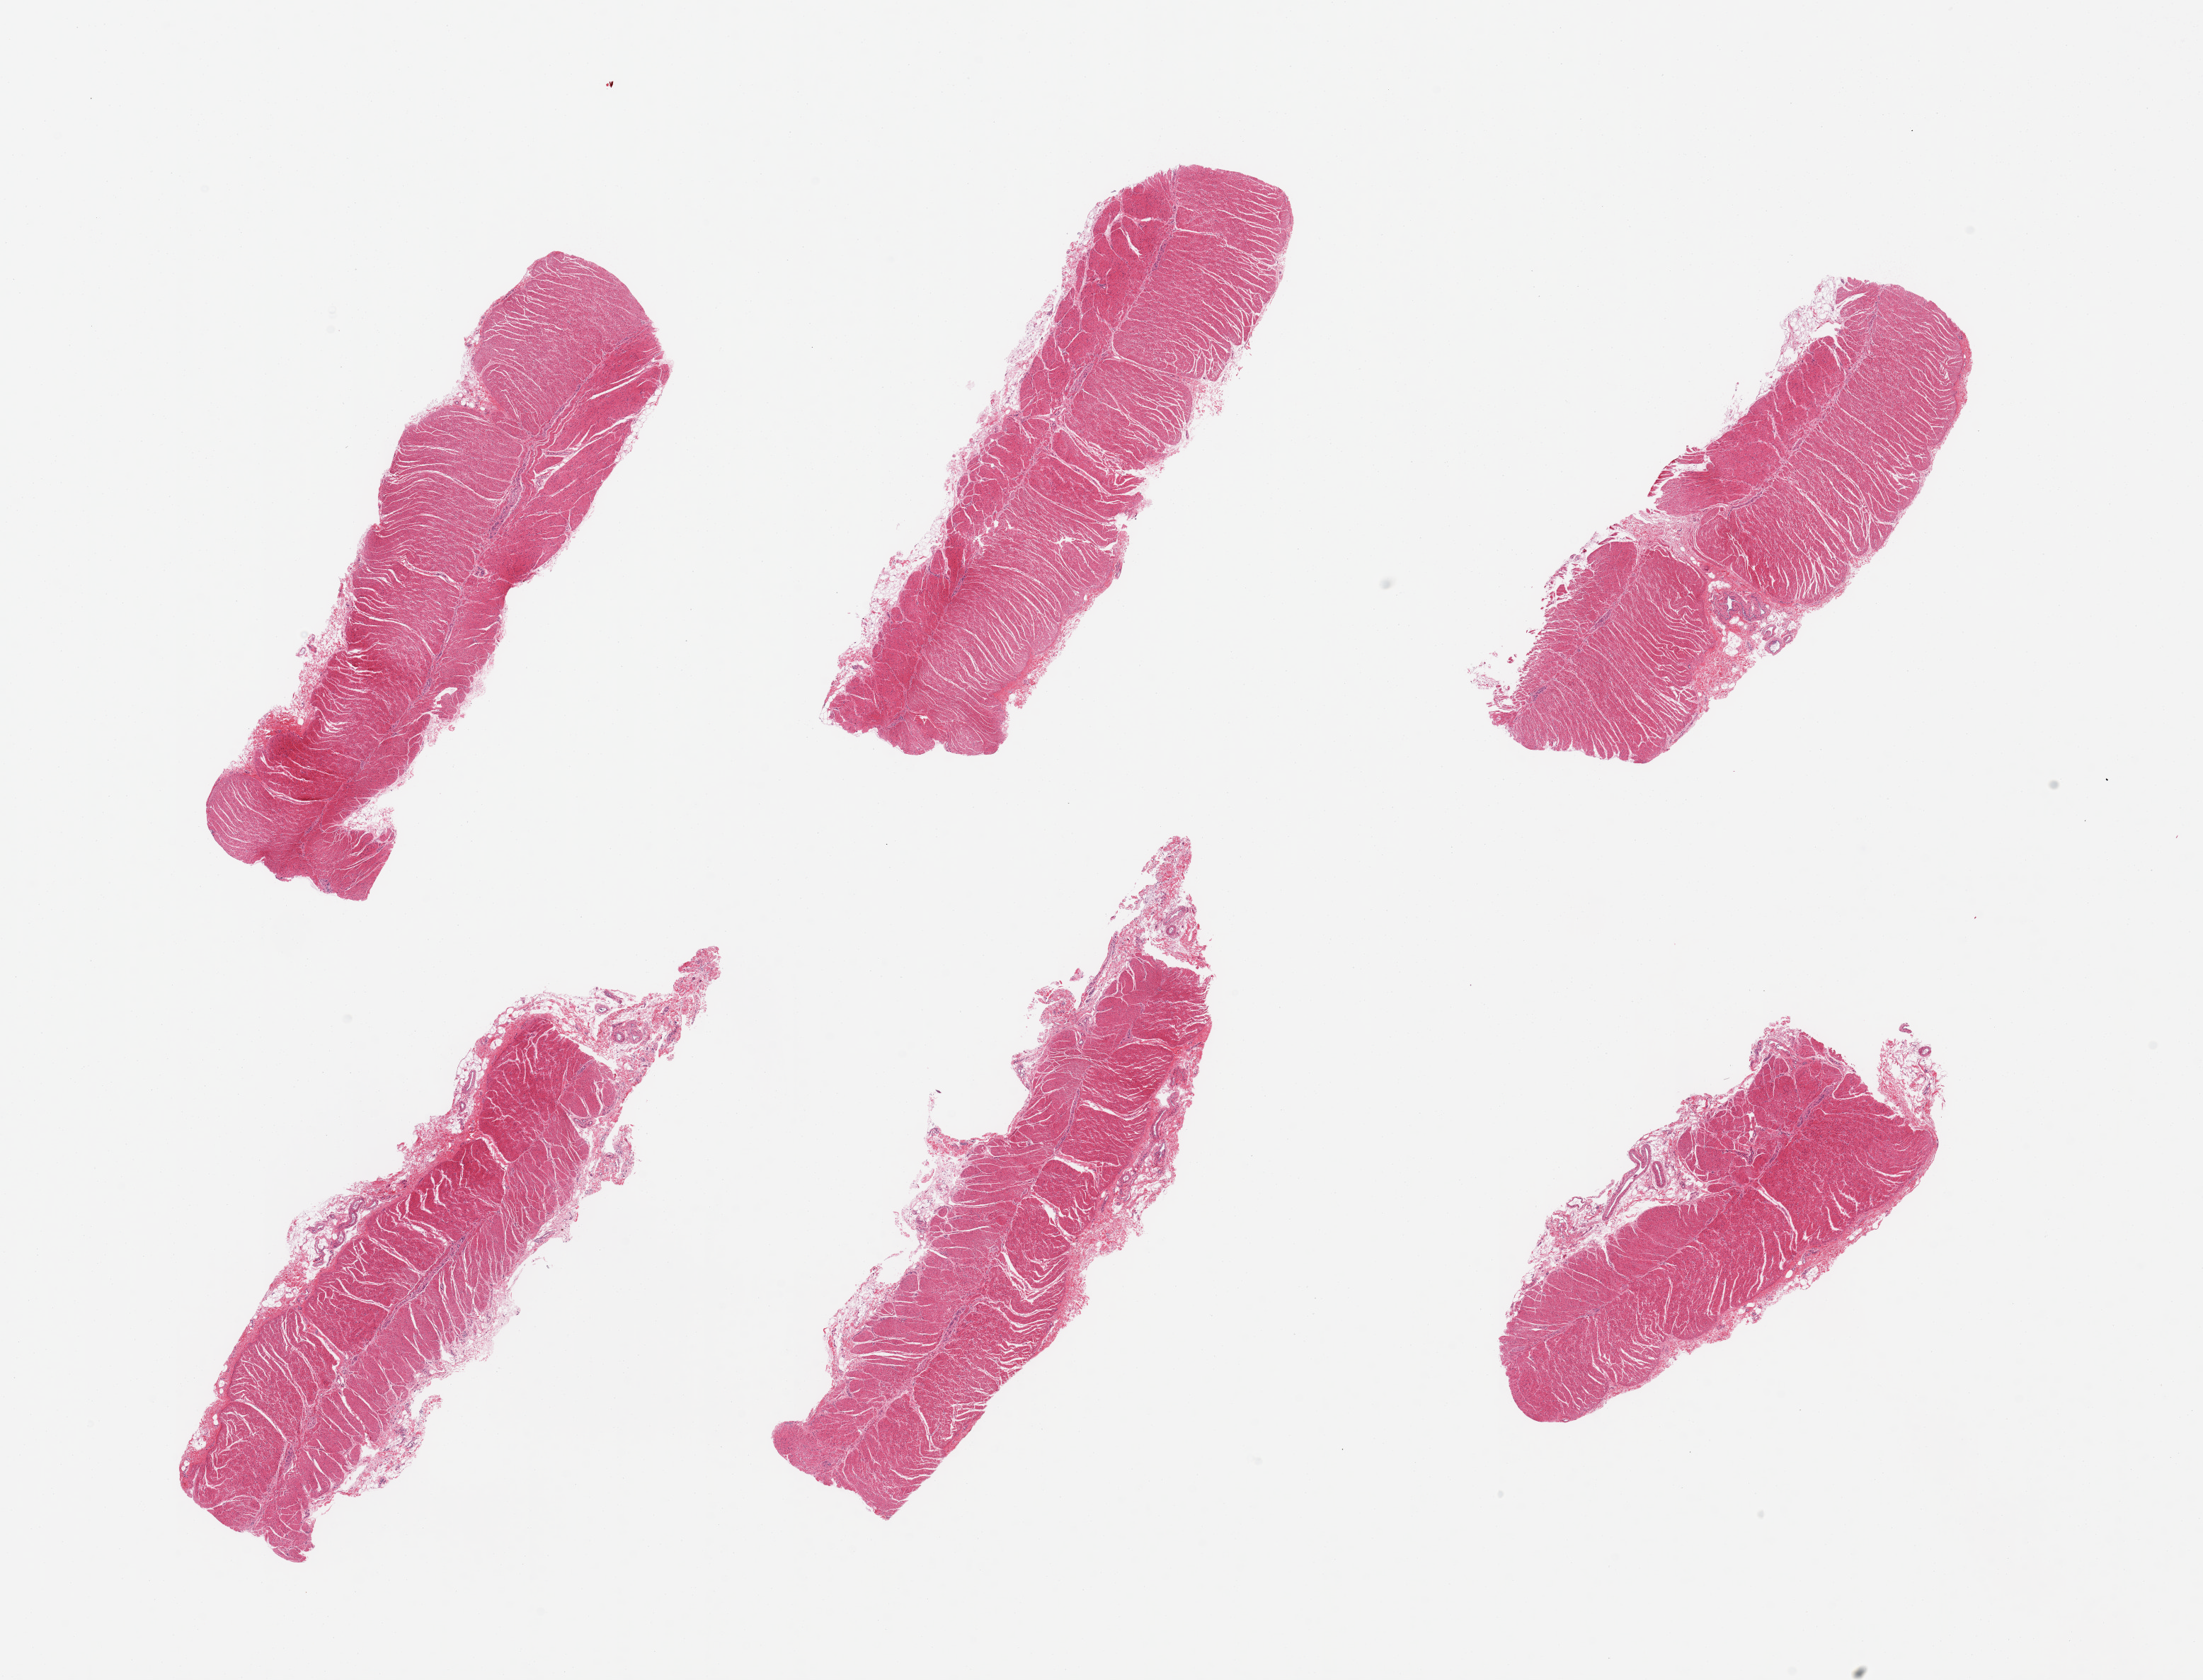
Hematoxylin and eosin (H&E) whole-slide image, brightfield — low-resolution overview of the scanned area, about 24.6 x 18.8 mm; PAXgene-fixed paraffin-embedded (PFPE) section; sampled site (target tissue): sigmoid colon; donor tissue sample.
• reviewer comment on this tissue sample: 6 pieces; target musculariss